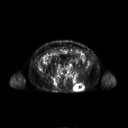
FDG PET of an extremity soft-tissue mass (from a PET/CT study), one axial slice. Position 92 of 267 along the scan axis. 3.27 mm slice thickness. 128 × 128 image matrix, field of view 700 × 700 mm. Male patient, age 61 years. From the clinical record (not read from this slice): histological type: pleiomorphic leiomyosarcoma; grade: high; site of the primary tumour: left buttock.
Outlined on this slice (expert contour drawn on MRI and transferred to this co-registered scan by the dataset authors):
- gross tumour volume including surrounding oedema: bounding box [x1, y1, x2, y2] px = [74, 84, 84, 92]
- gross tumour volume (mass): [74, 84, 83, 91]